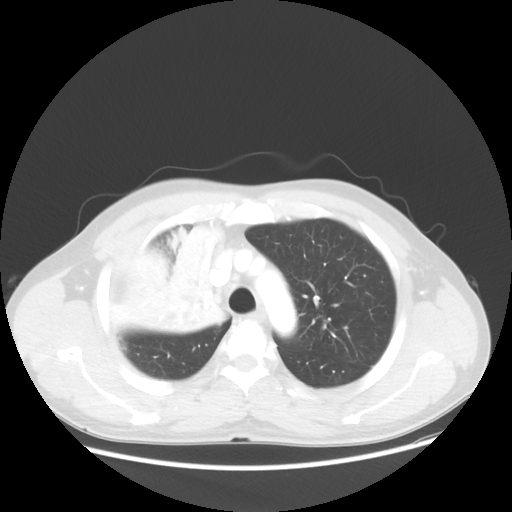
Chest CT, one axial slice; slice 41 of 56 in the series (ordered by position); lung window (W 1500 / L -600 HU); 5 mm slice thickness; 512 × 512 image matrix, field of view 398 × 398 mm. Patient: male, 60 years. From the clinical record (not read from this slice): clinical TNM (as recorded): T2a N1 M0.
Structures marked on this image (rectangle marked by the reading radiologist):
- lung tumour (recorded histology: squamous cell carcinoma): bounding box <148,224,234,343> (left, top, right, bottom; pixels)